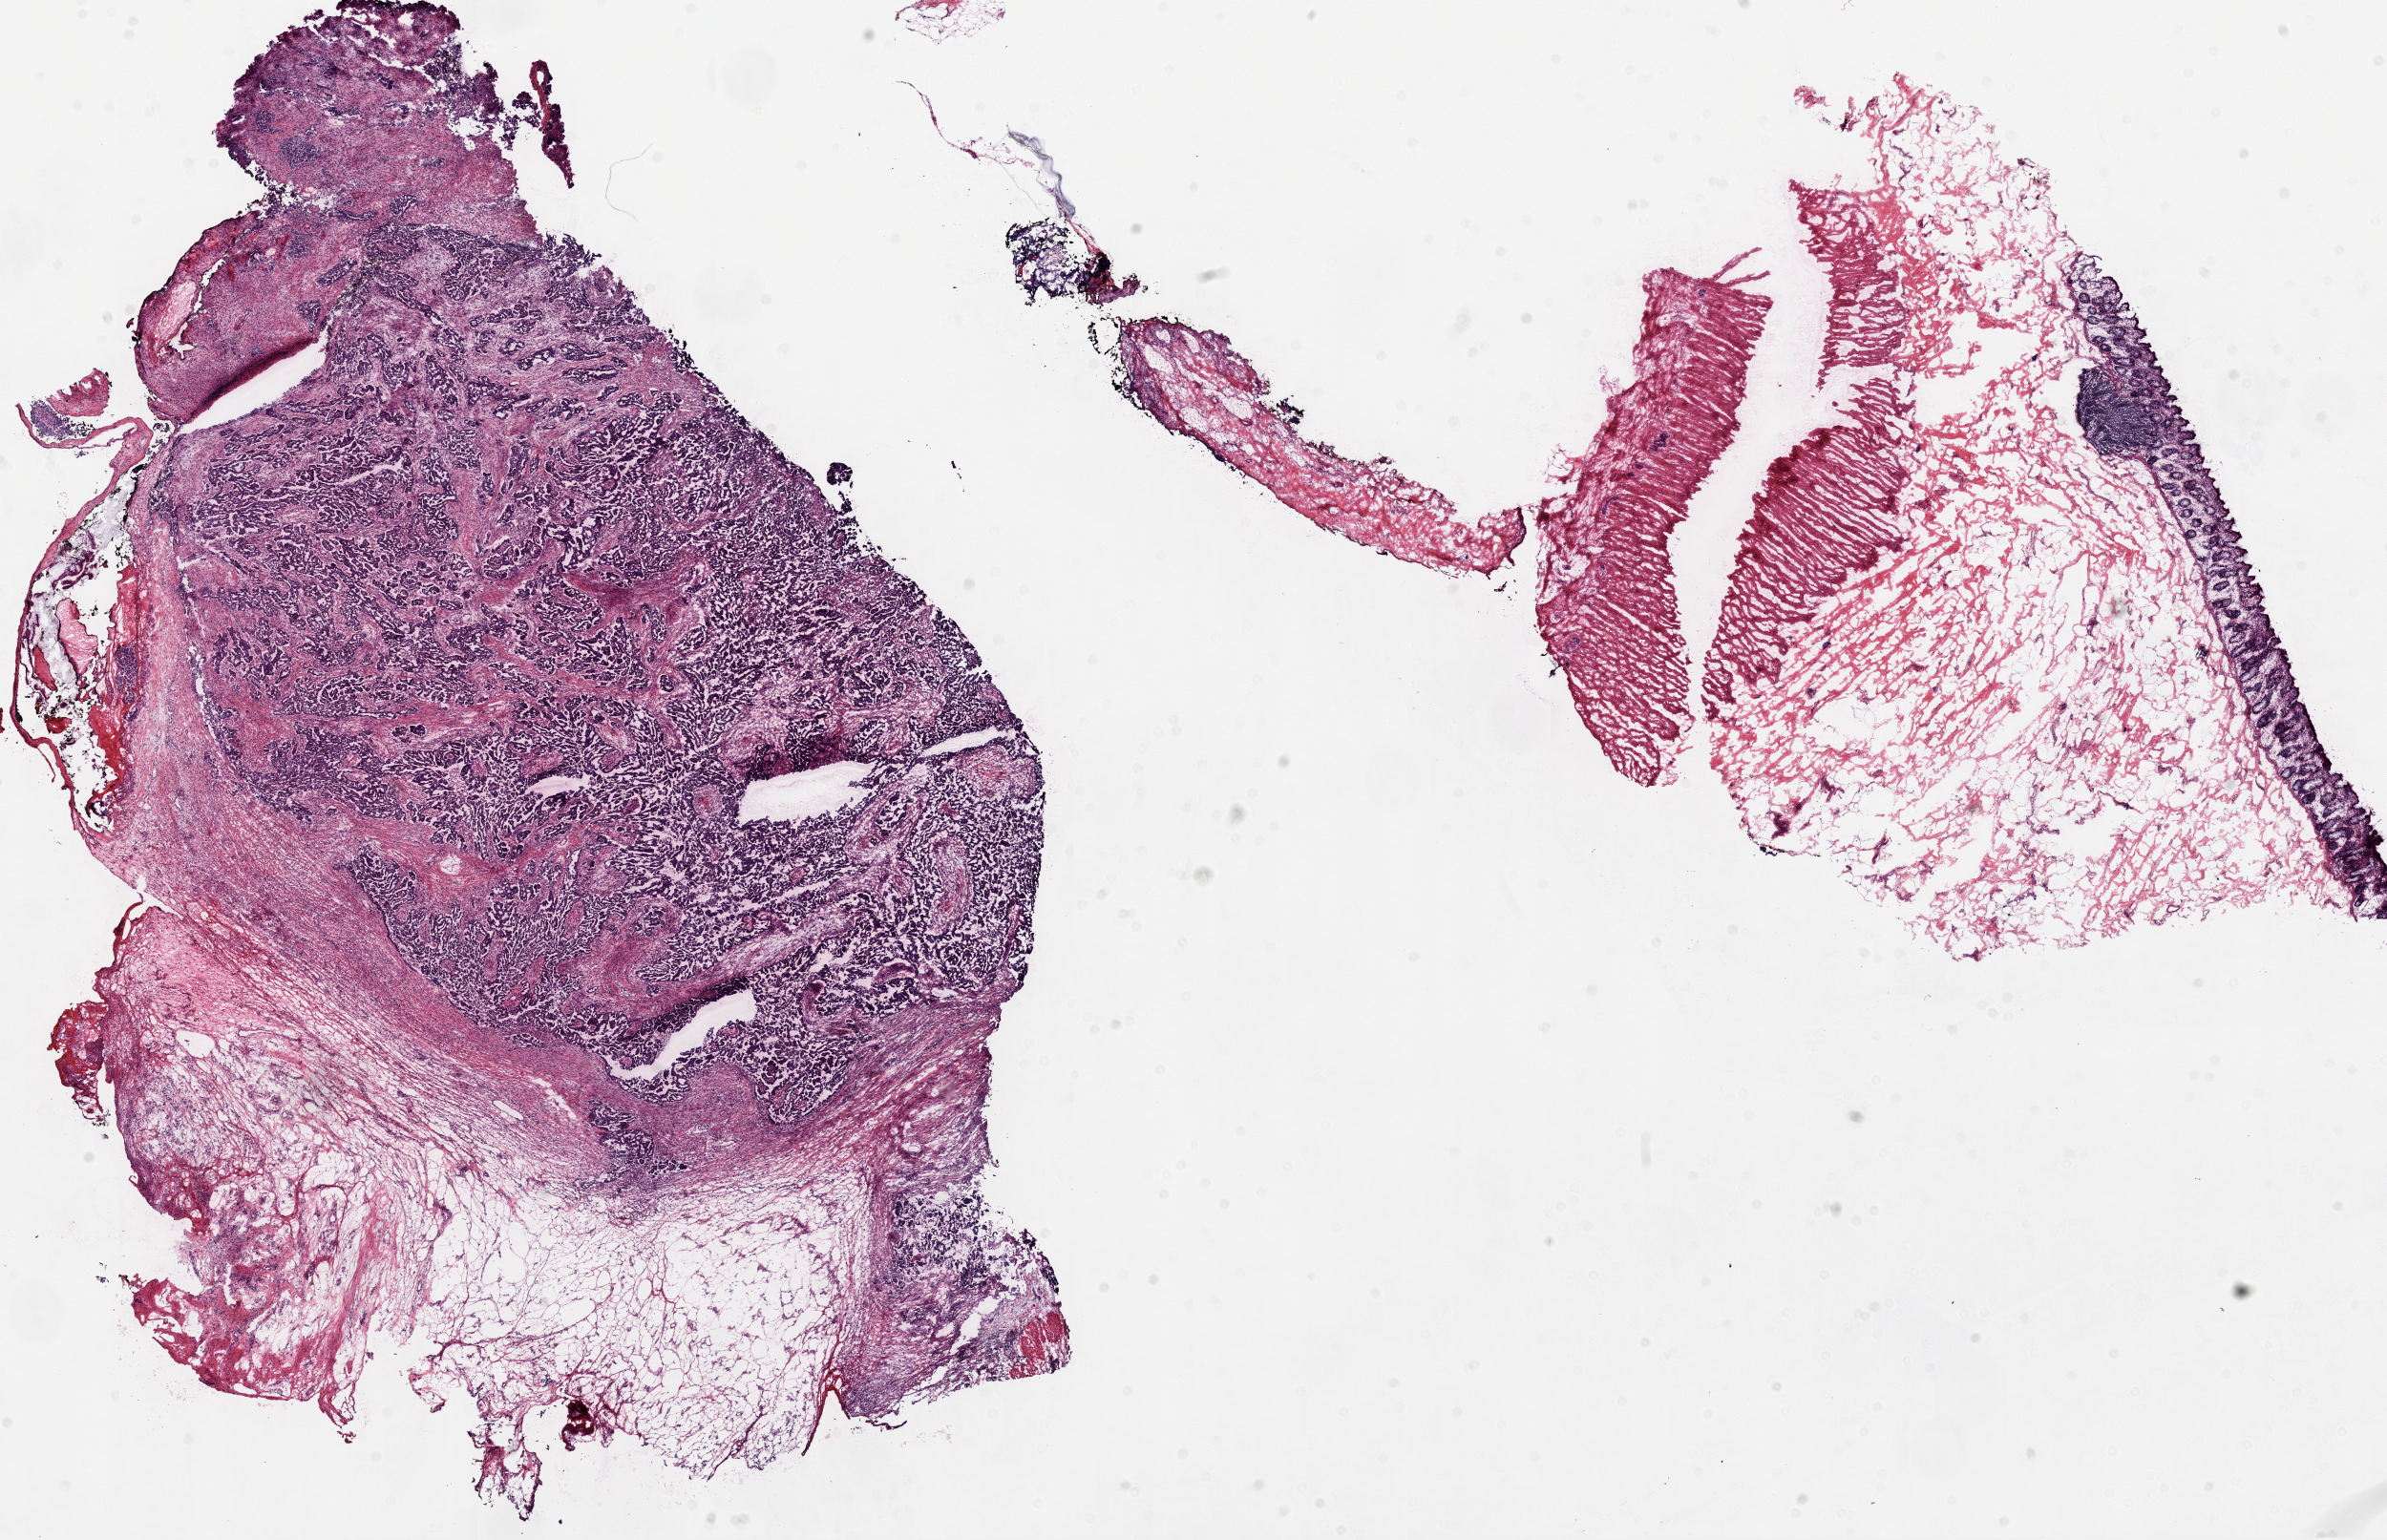
Hematoxylin and eosin (H&E) stained whole-slide image — whole scanned area (about 20.1 x 12.9 mm) shown as a low-resolution overview. Frozen section from the top of the tissue portion. Primary tumour sample from the ovary. Female patient; age at initial diagnosis 43 years. Histologic grade: G3 (poorly differentiated). Composition of this section per pathologist review: tumour cells 90%, tumour nuclei 90%, normal cells 0%, stromal cells 10%, necrosis 0%.
* pathologic diagnosis: Serous cystadenocarcinoma, NOS
* FIGO stage: IV
* laterality: bilateral